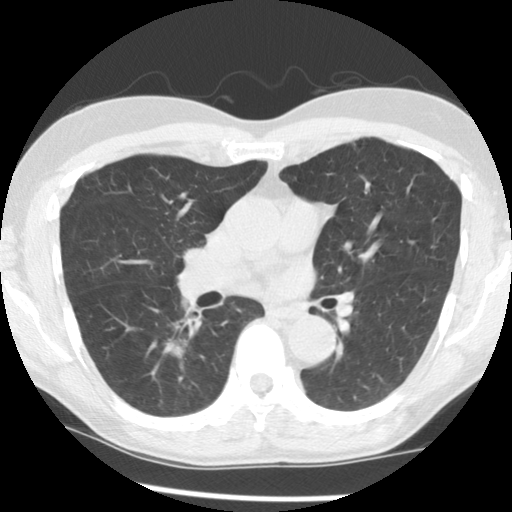
Low-dose screening chest CT, one axial slice. Slice 77 of 145 in the series (ordered by position). 140 kVp. Lung window (W 1500 / L -600 HU). 2.5 mm slice thickness. 512 × 512 image matrix.
Annotated regions visible in this slice (manually delineated by an expert):
- lesion 1 (tumor, lower lobe of right lung): bounding box <163,338,187,357> (left, top, right, bottom; pixels)